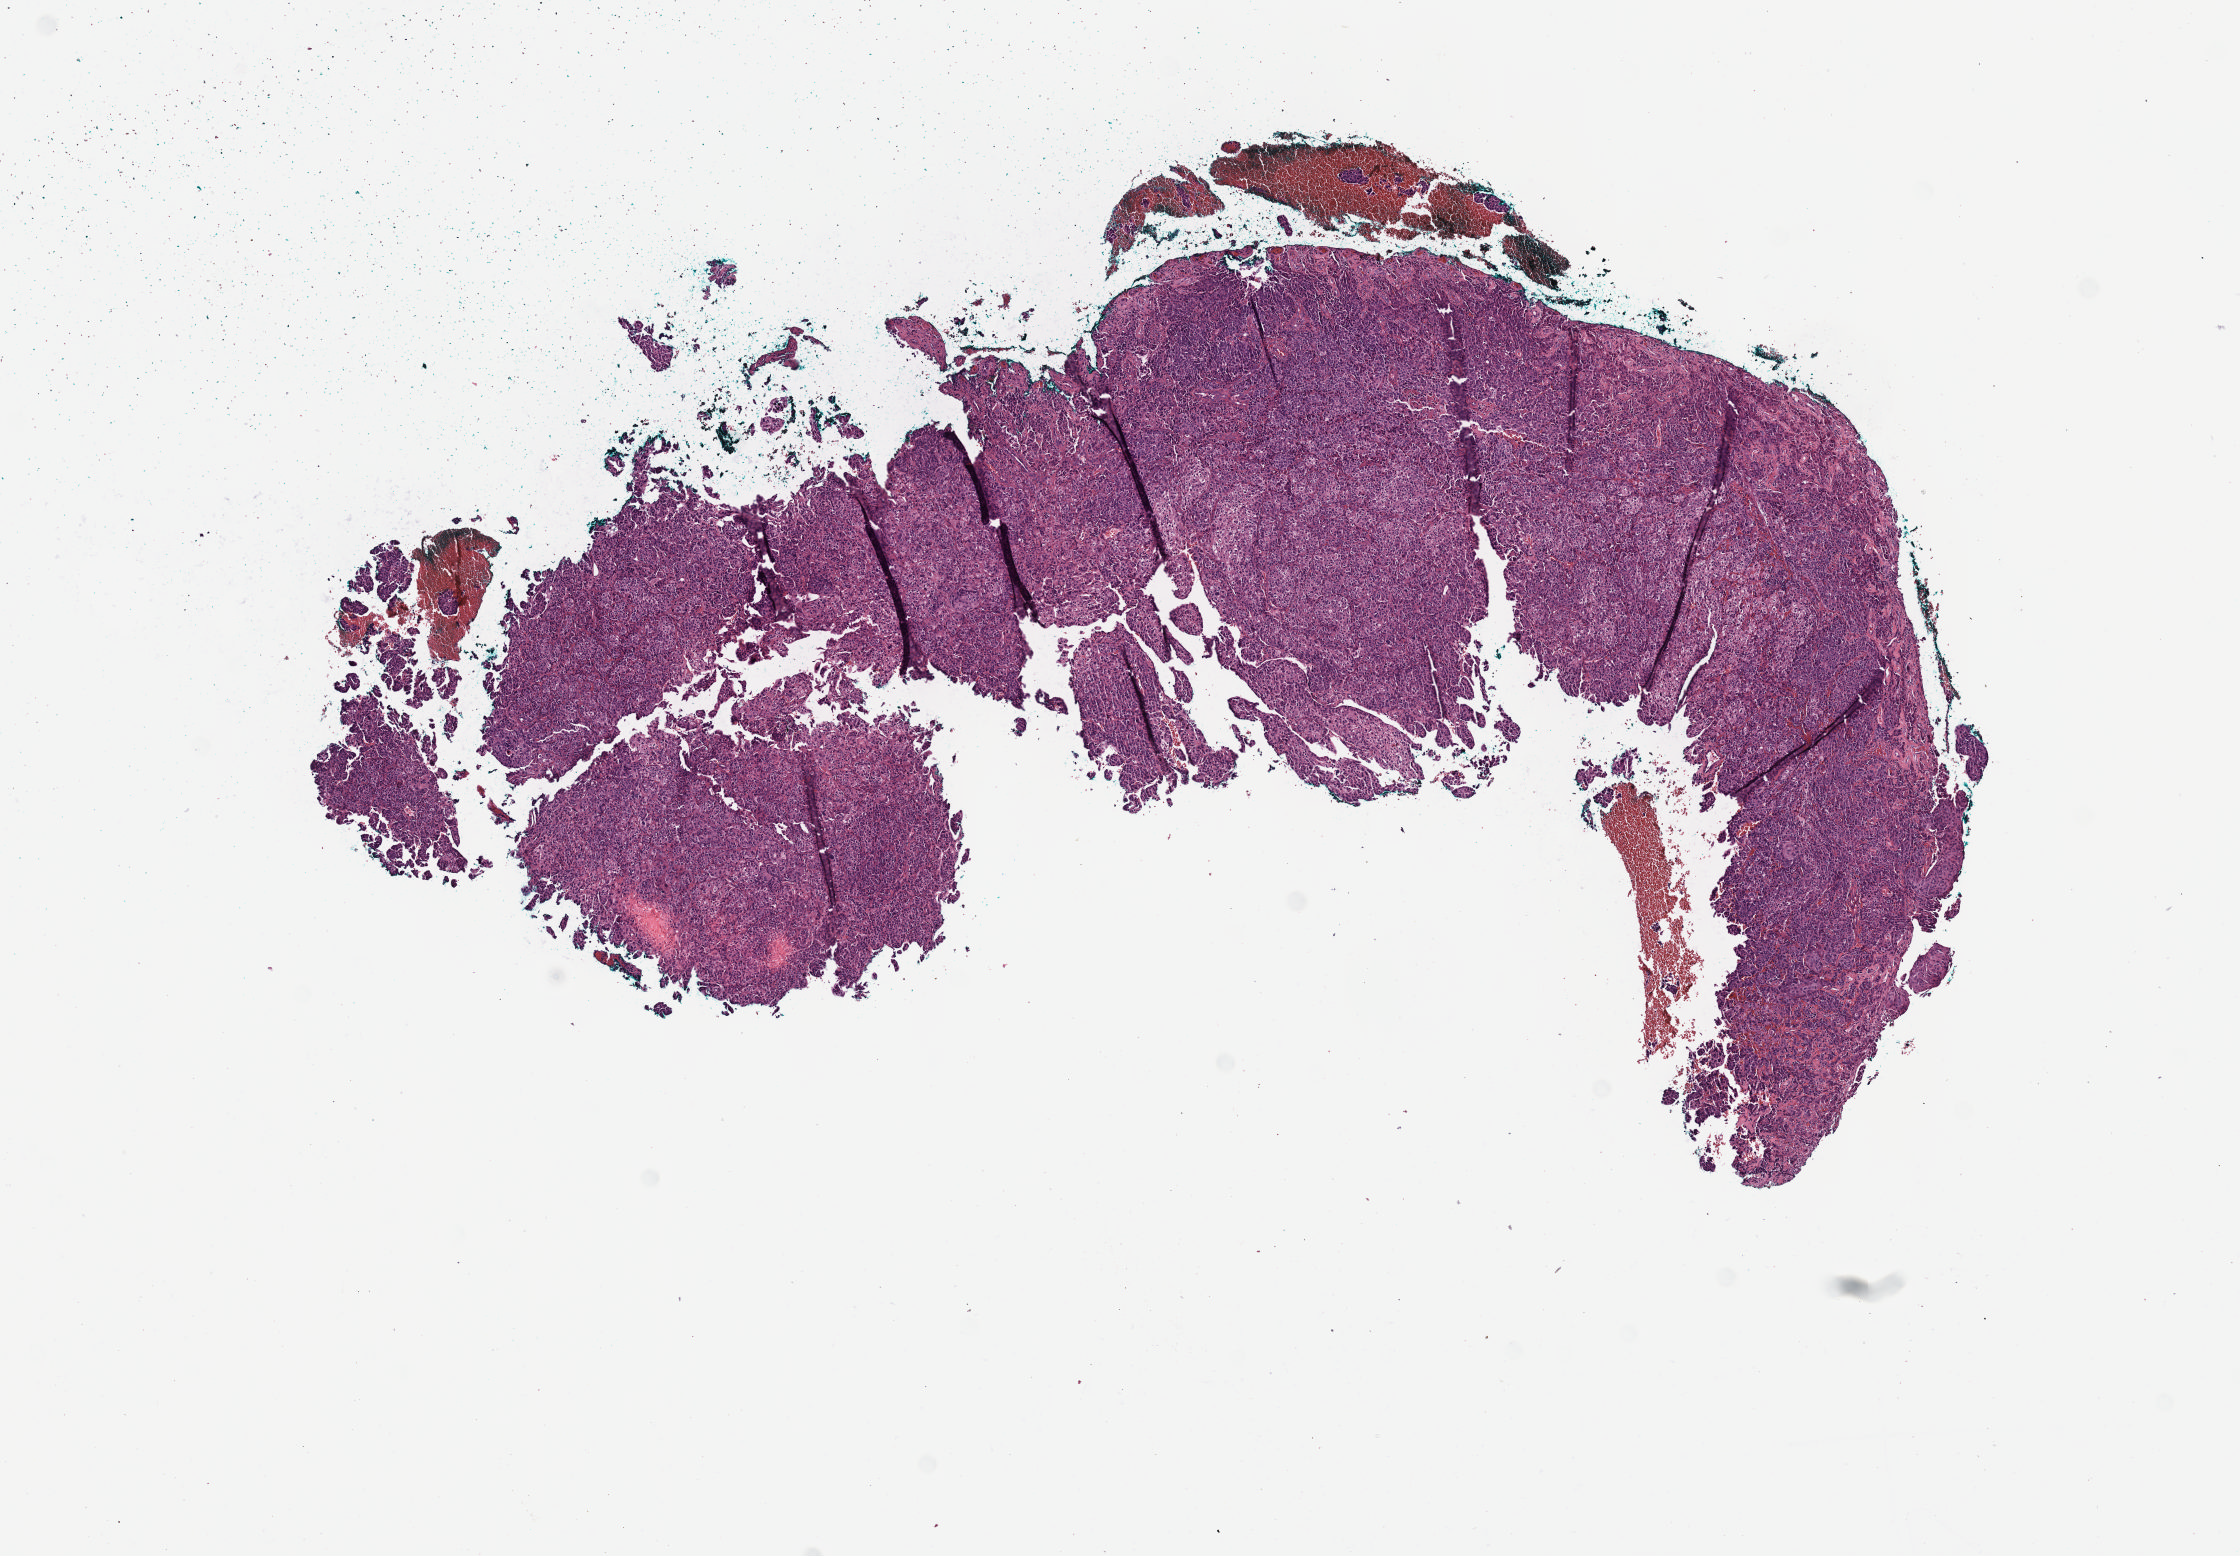
Whole-slide histology image, H&E, shown as a low-resolution overview of the whole scanned area (about 9.1 x 6.3 mm, slide scanned at 40x). Formalin-fixed paraffin-embedded (FFPE) diagnostic section. Primary tumour sample from the cervix. Female patient; age at initial diagnosis 32 years. Histologic grade: G2 (moderately differentiated).
FIGO stage: IIB. Histologic diagnosis: Squamous cell carcinoma, NOS (cervix uteri).